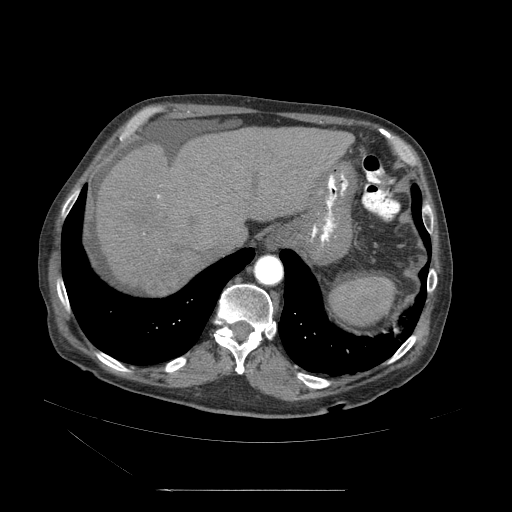
Contrast-enhanced abdominal CT (liver protocol), one axial slice; reconstruction kernel STANDARD; 120 kVp; soft-tissue window (W 400 / L 40 HU); 512 × 512 image matrix, field of view 440 × 440 mm. From the clinical record (not read from this slice): diagnosis: hepatocellular carcinoma (patient treated with transarterial chemoembolisation; whether this scan precedes or follows treatment is not stated here); TNM stage (as recorded): Stage-II; Child-Pugh class: A; tumour nodularity: multinodular.
Annotated regions visible in this slice (semi-automatic segmentation, software-assisted and operator-edited):
- abdominal aorta: bounding box (x1, y1, x2, y2) in pixels: (254, 256, 284, 288)
- liver parenchyma outside the tumour (the mass and vessels are separate outlines, so this box may not span the whole liver): (91, 128, 355, 296)
- mass: (143, 265, 188, 303)
- liver vessels: (108, 199, 234, 265)